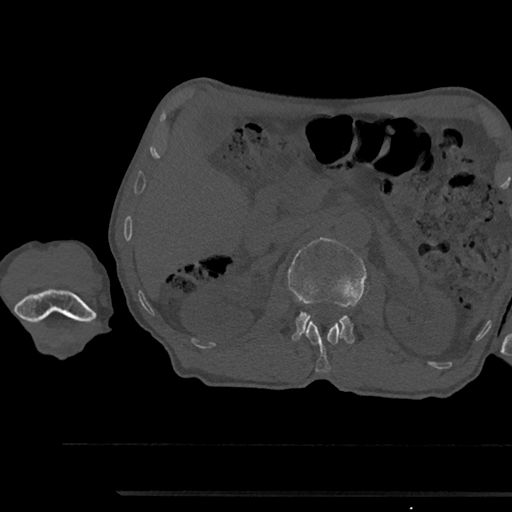
CT including the spine, one axial slice; position 601 of 797 along the scan axis; reconstruction kernel Br40s/3; 120 kVp; bone window (W 1800 / L 400 HU); 0.5 mm slice thickness; 512 × 512 image matrix, field of view 367 × 367 mm. Male patient, age 79 years. Case-level facts recorded for this patient, not image findings: primary cancer: prostate.
Annotated regions visible in this slice (semi-automatic segmentation, software-assisted and operator-edited):
- L1 vertebra: box from (x=305, y=321) to (x=342, y=372) px
- L2 vertebra: (x=288, y=238)–(x=368, y=344)